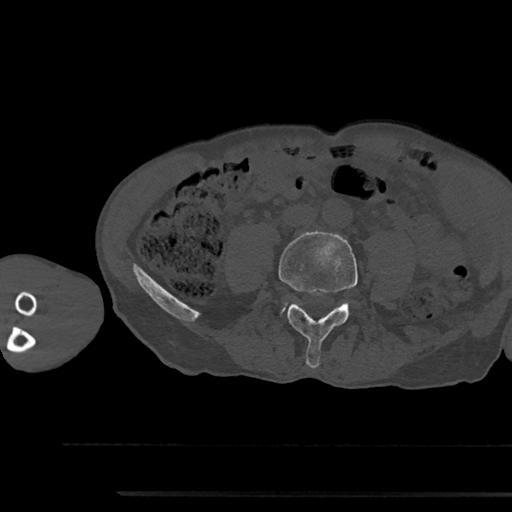
CT including the spine, one axial slice; slice 401 of 797 in the series (ordered by position); bone window (W 1800 / L 400 HU); 0.5 mm slice thickness; 512 × 512 image matrix, field of view 367 × 367 mm. Patient: male, 79 years. Case-level facts recorded for this patient, not image findings: primary cancer: prostate.
Annotated regions visible in this slice (semi-automatically segmented with operator editing):
- L4 vertebra: box from (x=279, y=231) to (x=358, y=368) px